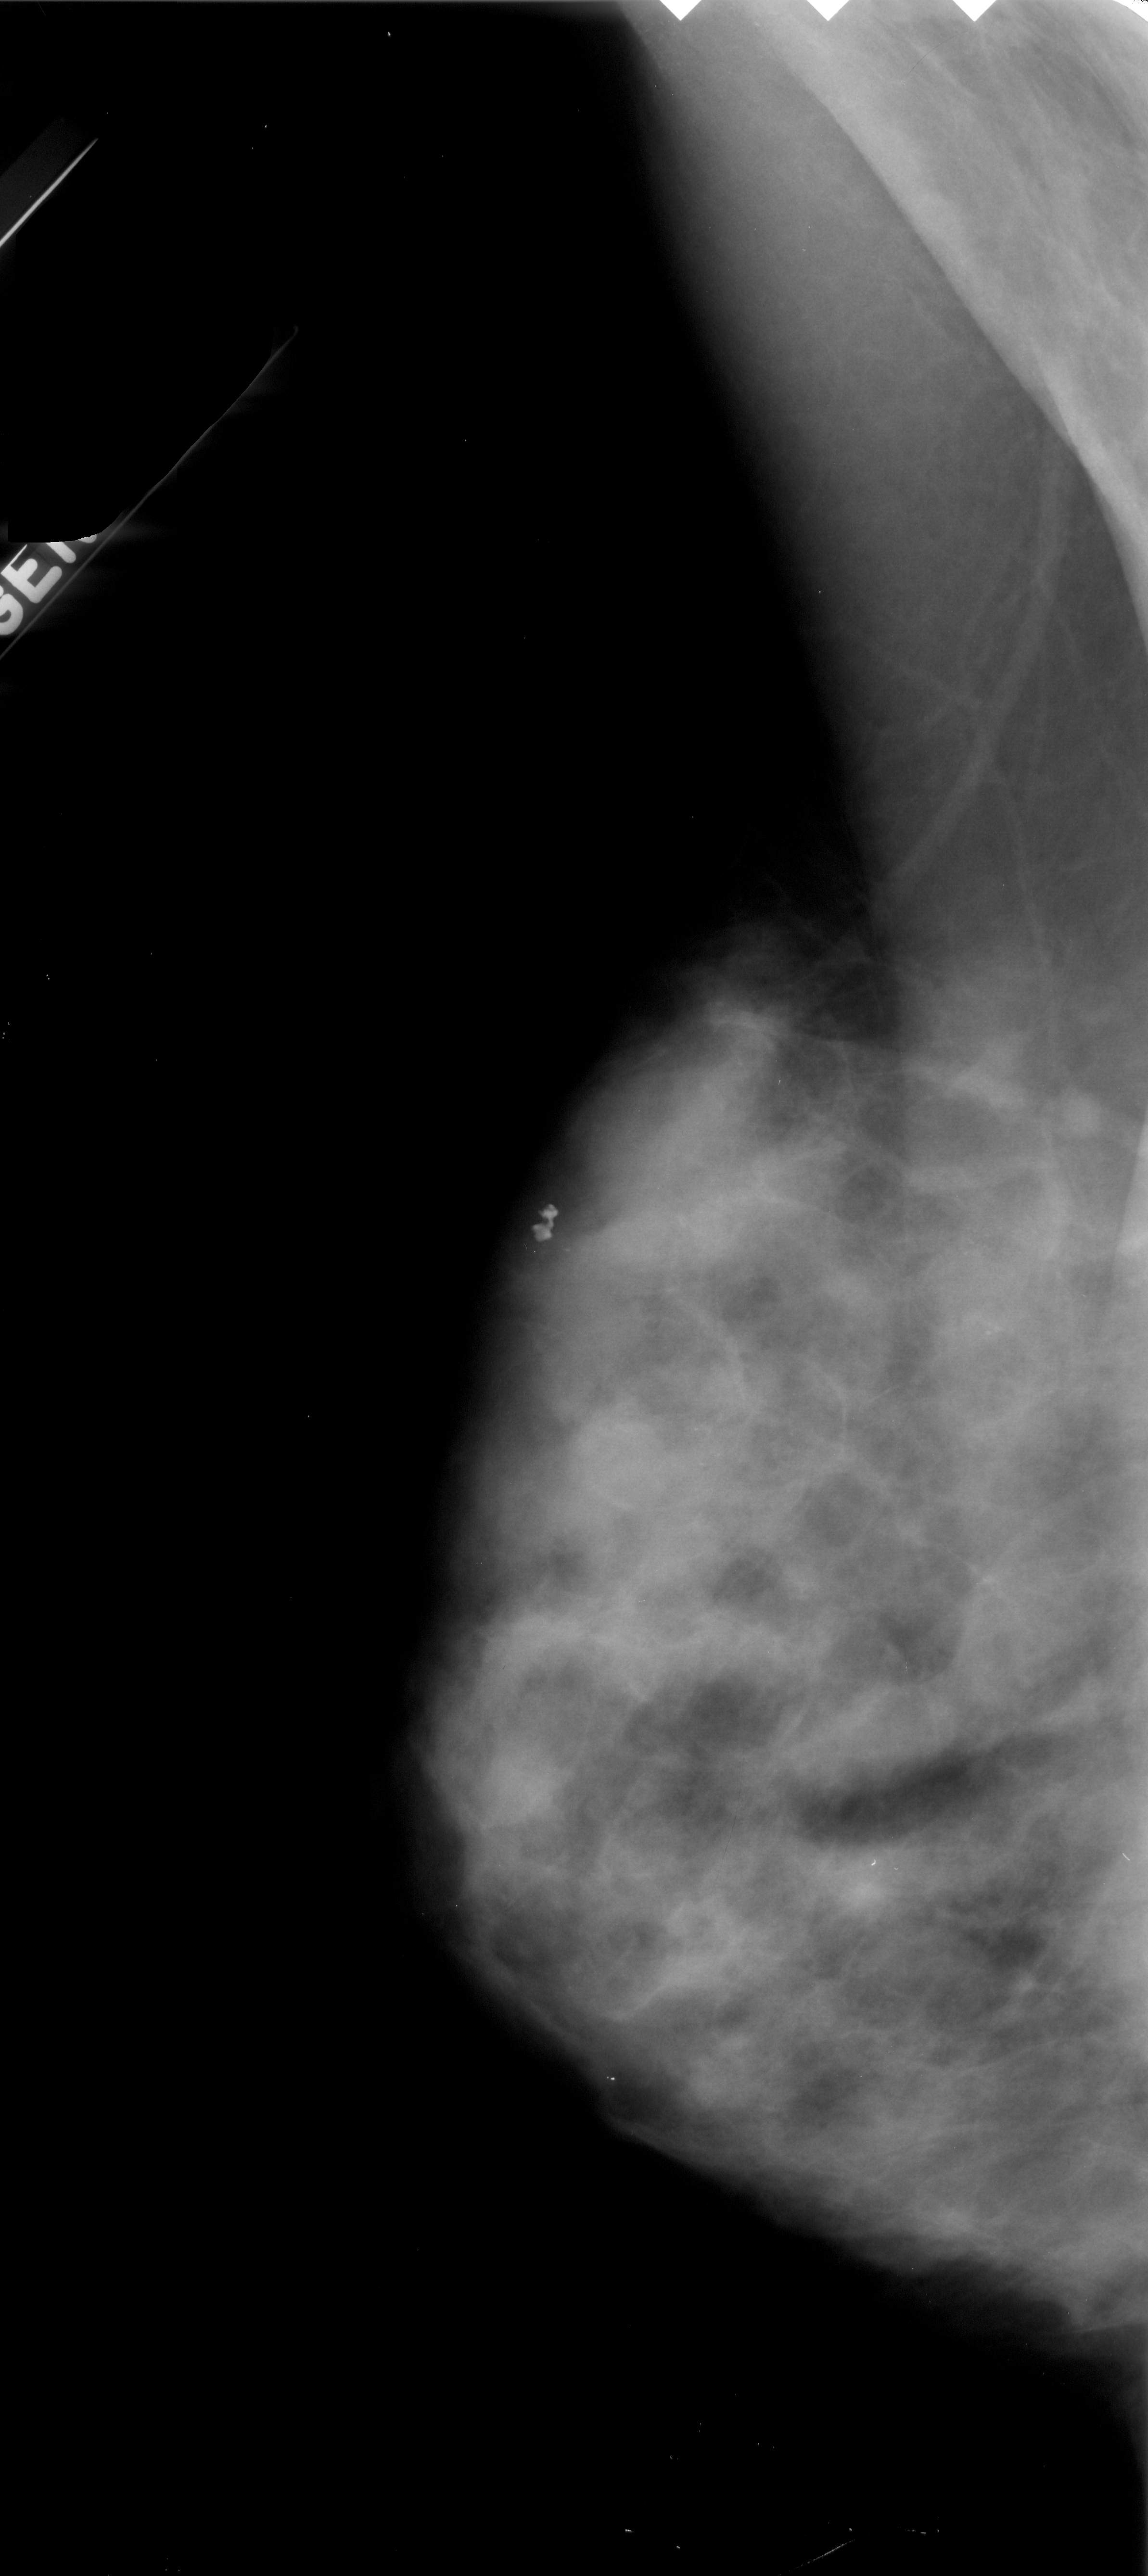
Scanned film-screen mammogram. Left breast. Mediolateral oblique (MLO) view. BI-RADS breast density category 4 (scale 1–4). 1148 × 2576 image matrix.
Expert-marked regions of interest on this image (one box per marked abnormality):
- calcifications, morphology pleomorphic, distribution clustered; BI-RADS assessment category 4; subtlety rating 1 on a 1 (subtle) to 5 (obvious) scale; pathology (as recorded): malignant: bounding box <934,1186,1056,1370> (left, top, right, bottom; pixels)